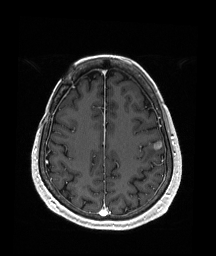
Brain MRI from a brain-tumour surgery series, one axial slice. Slice 62 of 176 in the series (ordered by position). T1-weighted post-contrast. 216 × 256 image matrix. Case-level facts recorded for this patient, not image findings: histopathology: Metastatic Malignant Melanoma; tumour location: Left Frontal.
Structures marked on this image (outlined manually by an expert reader):
- tumour: box from (x=152, y=141) to (x=162, y=150) px